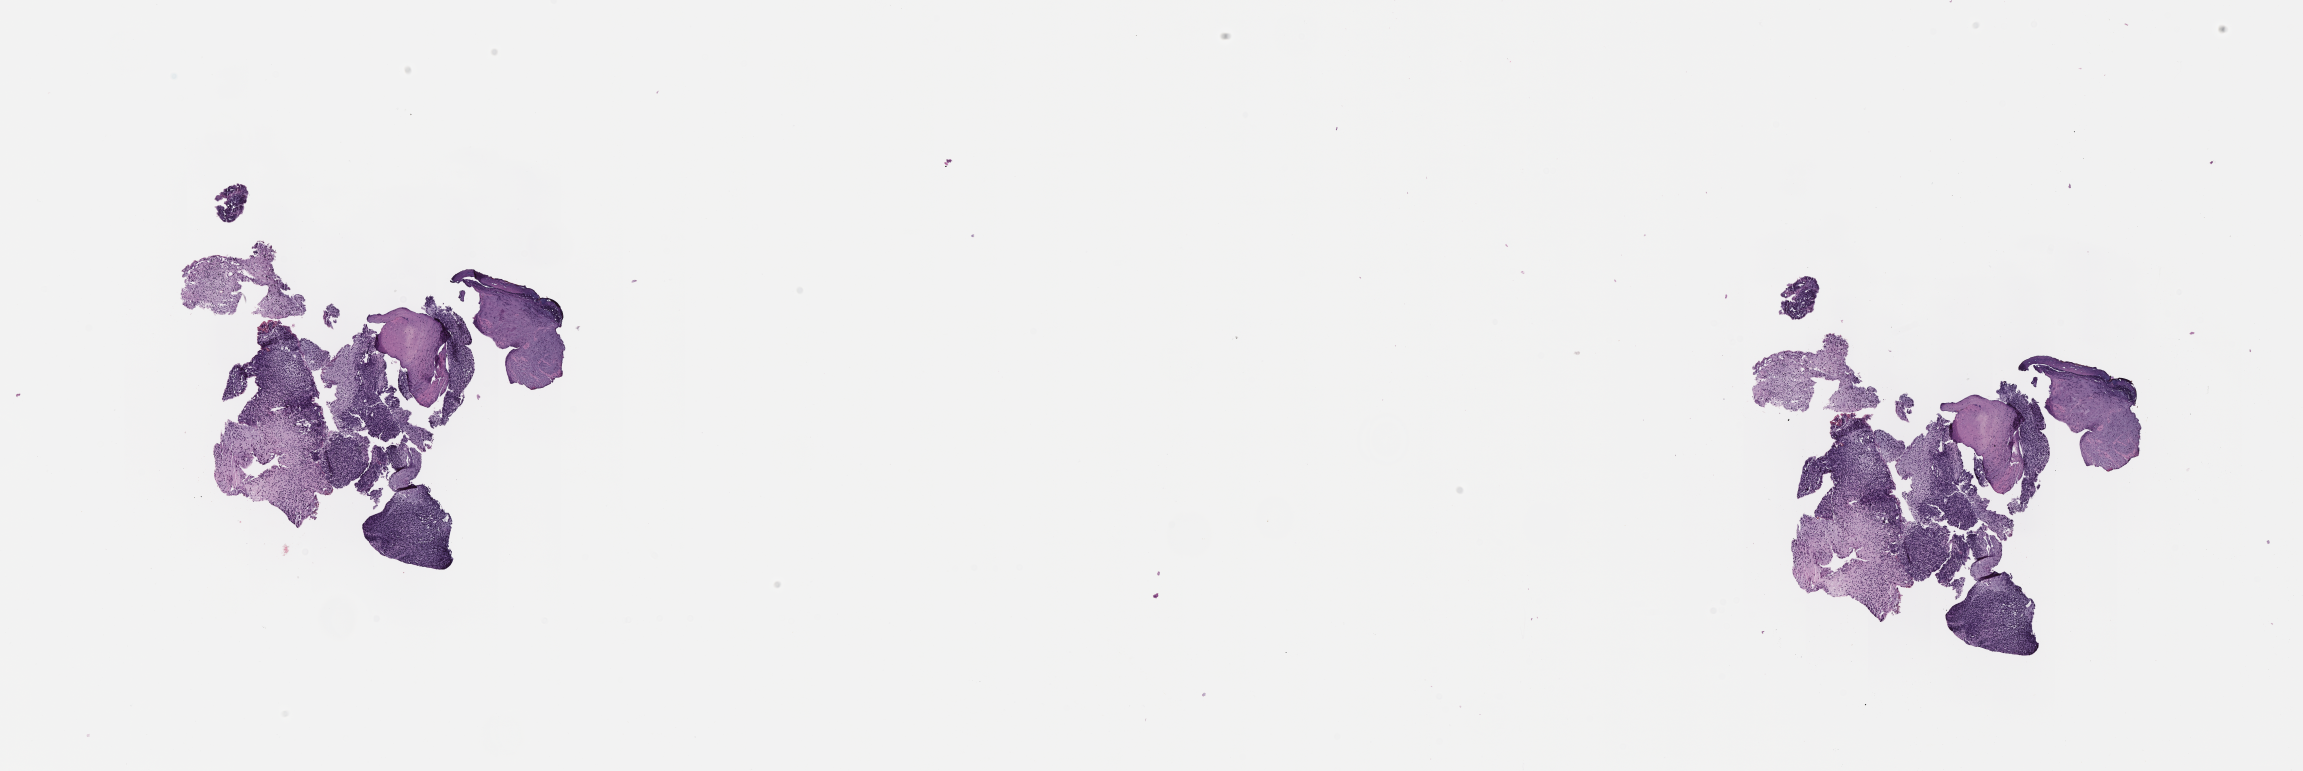
Whole-slide image, hematoxylin and eosin (H&E) stain of tumor tissue — low-resolution overview of the scanned area, about 18.6 x 6.2 mm. Formalin-fixed, paraffin-embedded (FFPE) tissue. Site: prostate. Patient: male, age 7.2 years at diagnosis.
- metastatic status at presentation (as recorded): non-metastatic
- diagnosis: rhabdomyosarcoma; histological classification: embryonal rhabdomyosarcoma
- stage (as recorded): 3